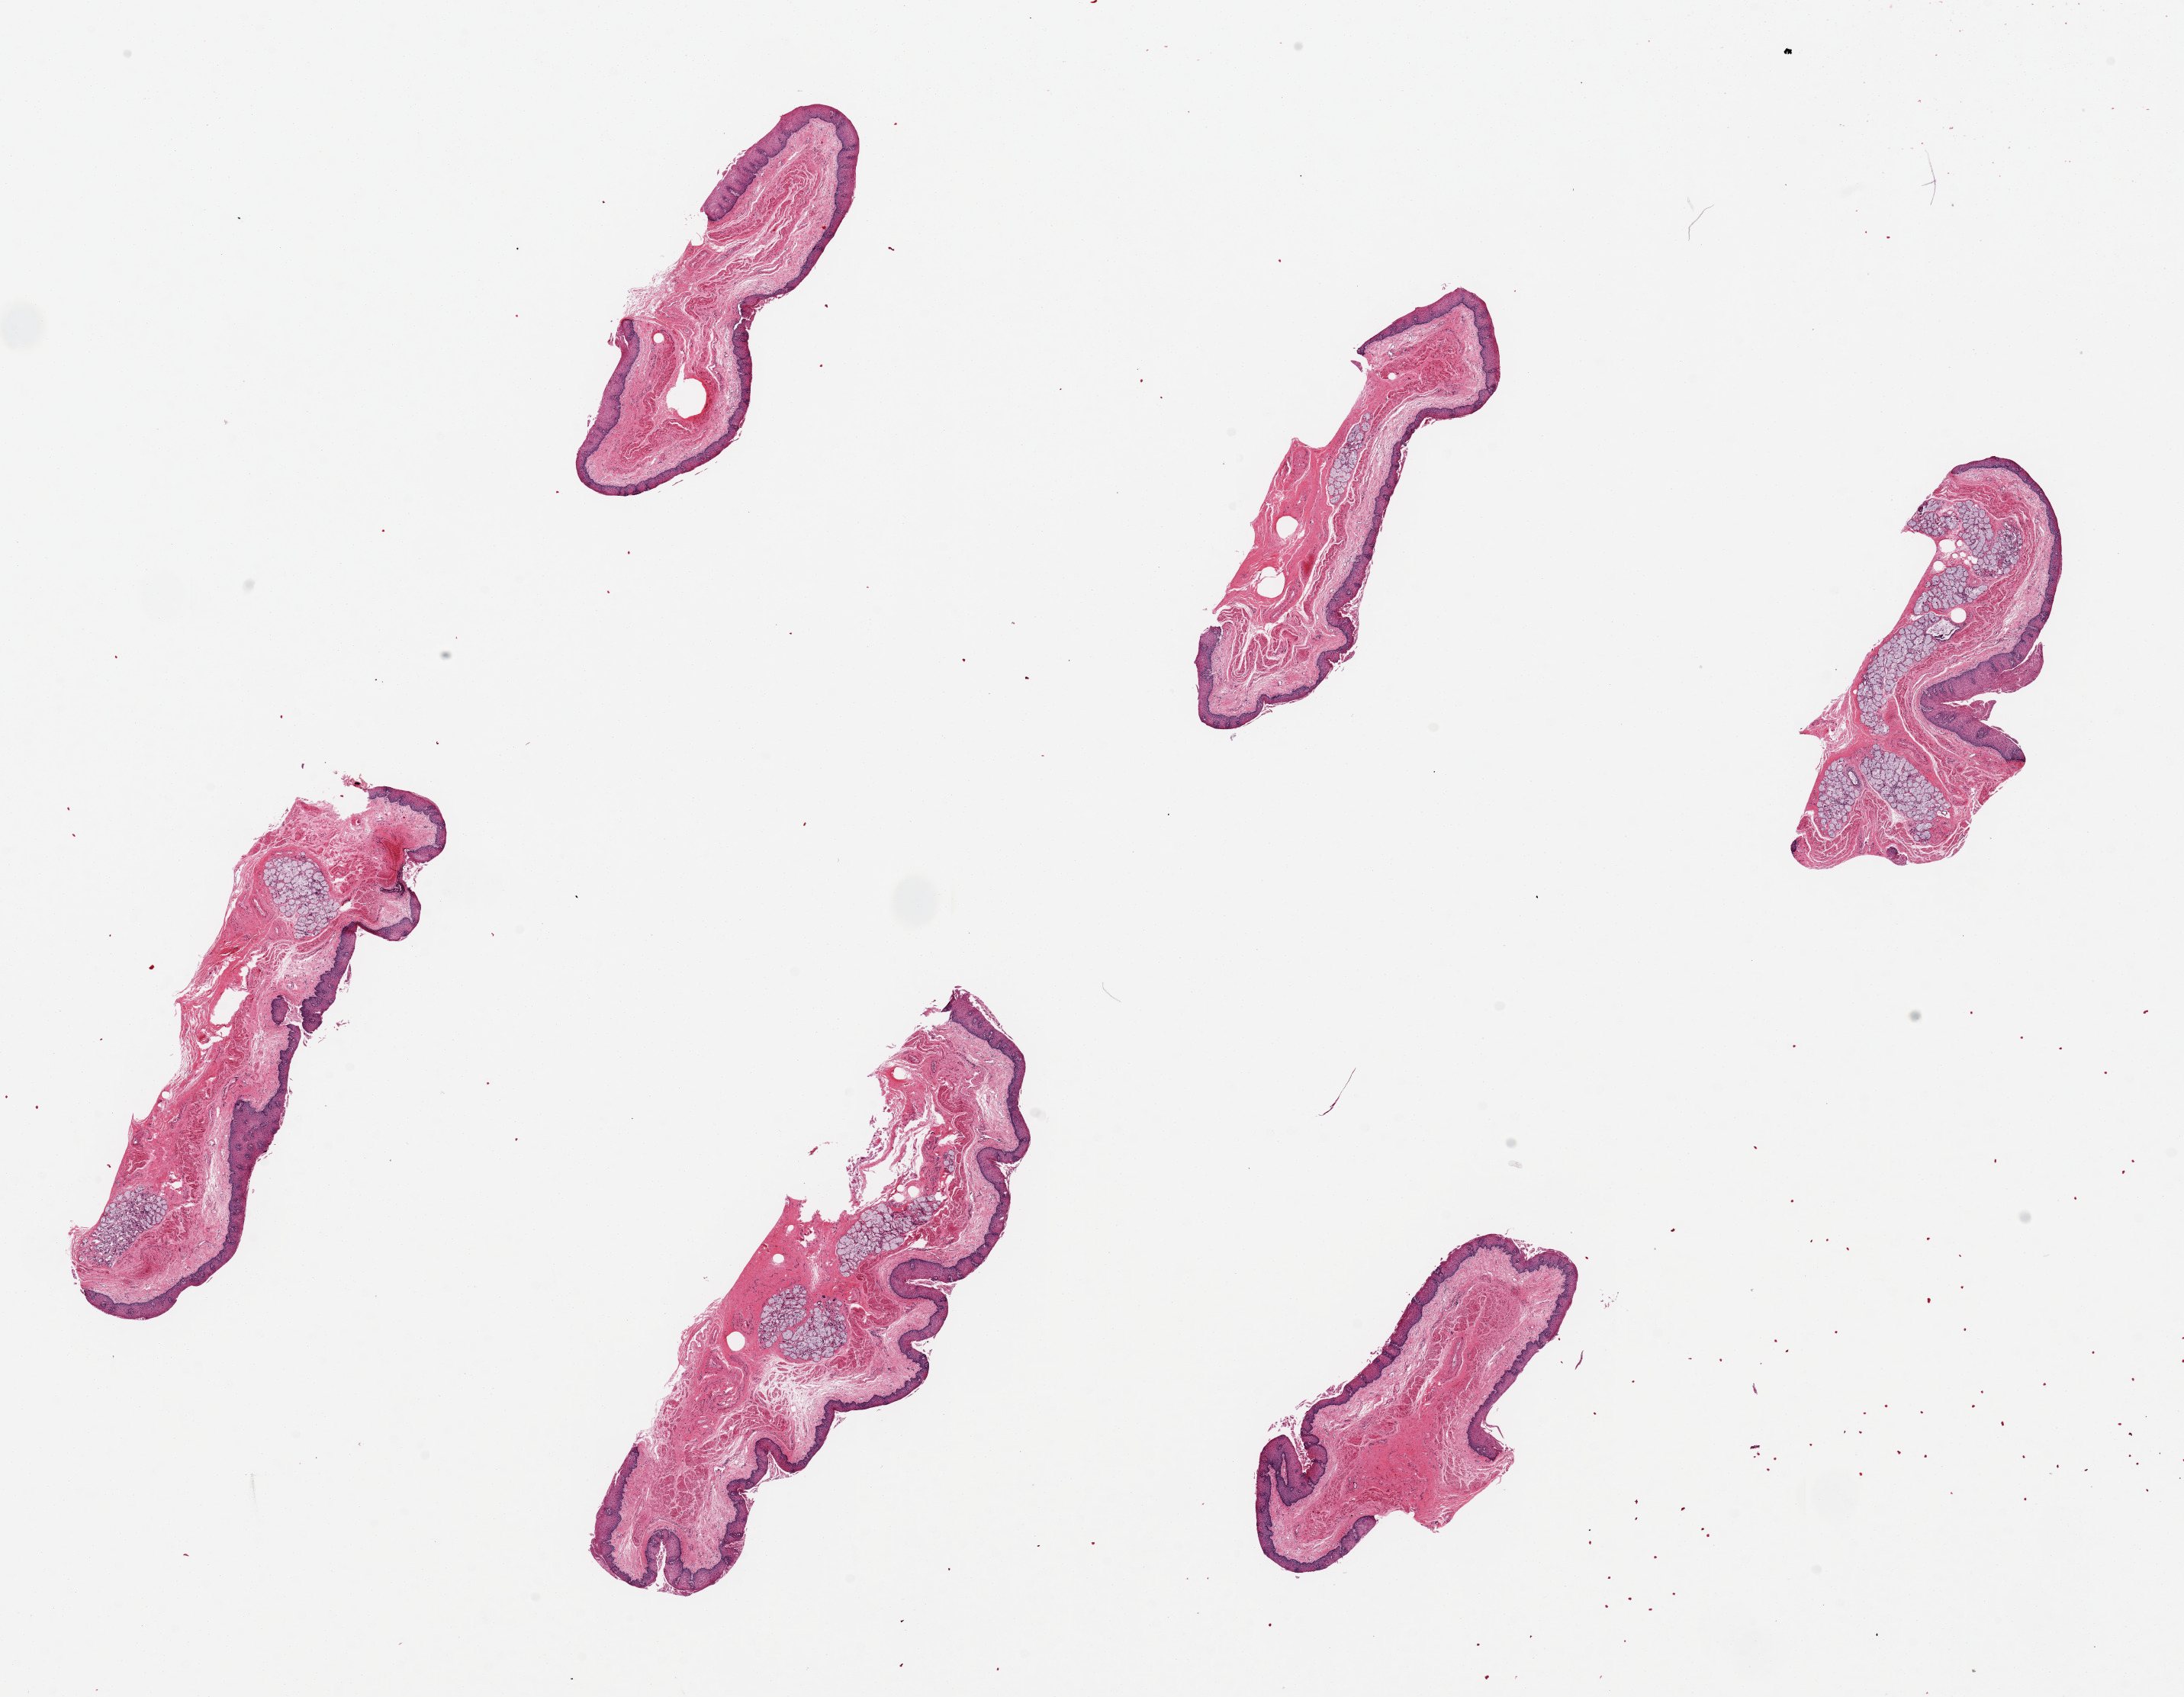
Whole-slide image, H&E stain — whole scanned area (about 22.6 x 17.6 mm, from a 20x scan) shown as a low-resolution overview, PAXgene-fixed paraffin-embedded (PFPE) section, sampled site (target tissue): esophageal mucous membrane, donor tissue sample. Donor: male.
Review note (as recorded): 6 pieces up to 7x2 mm; squamous mucosa well preserved; submucosal glands moderately autolyzed.